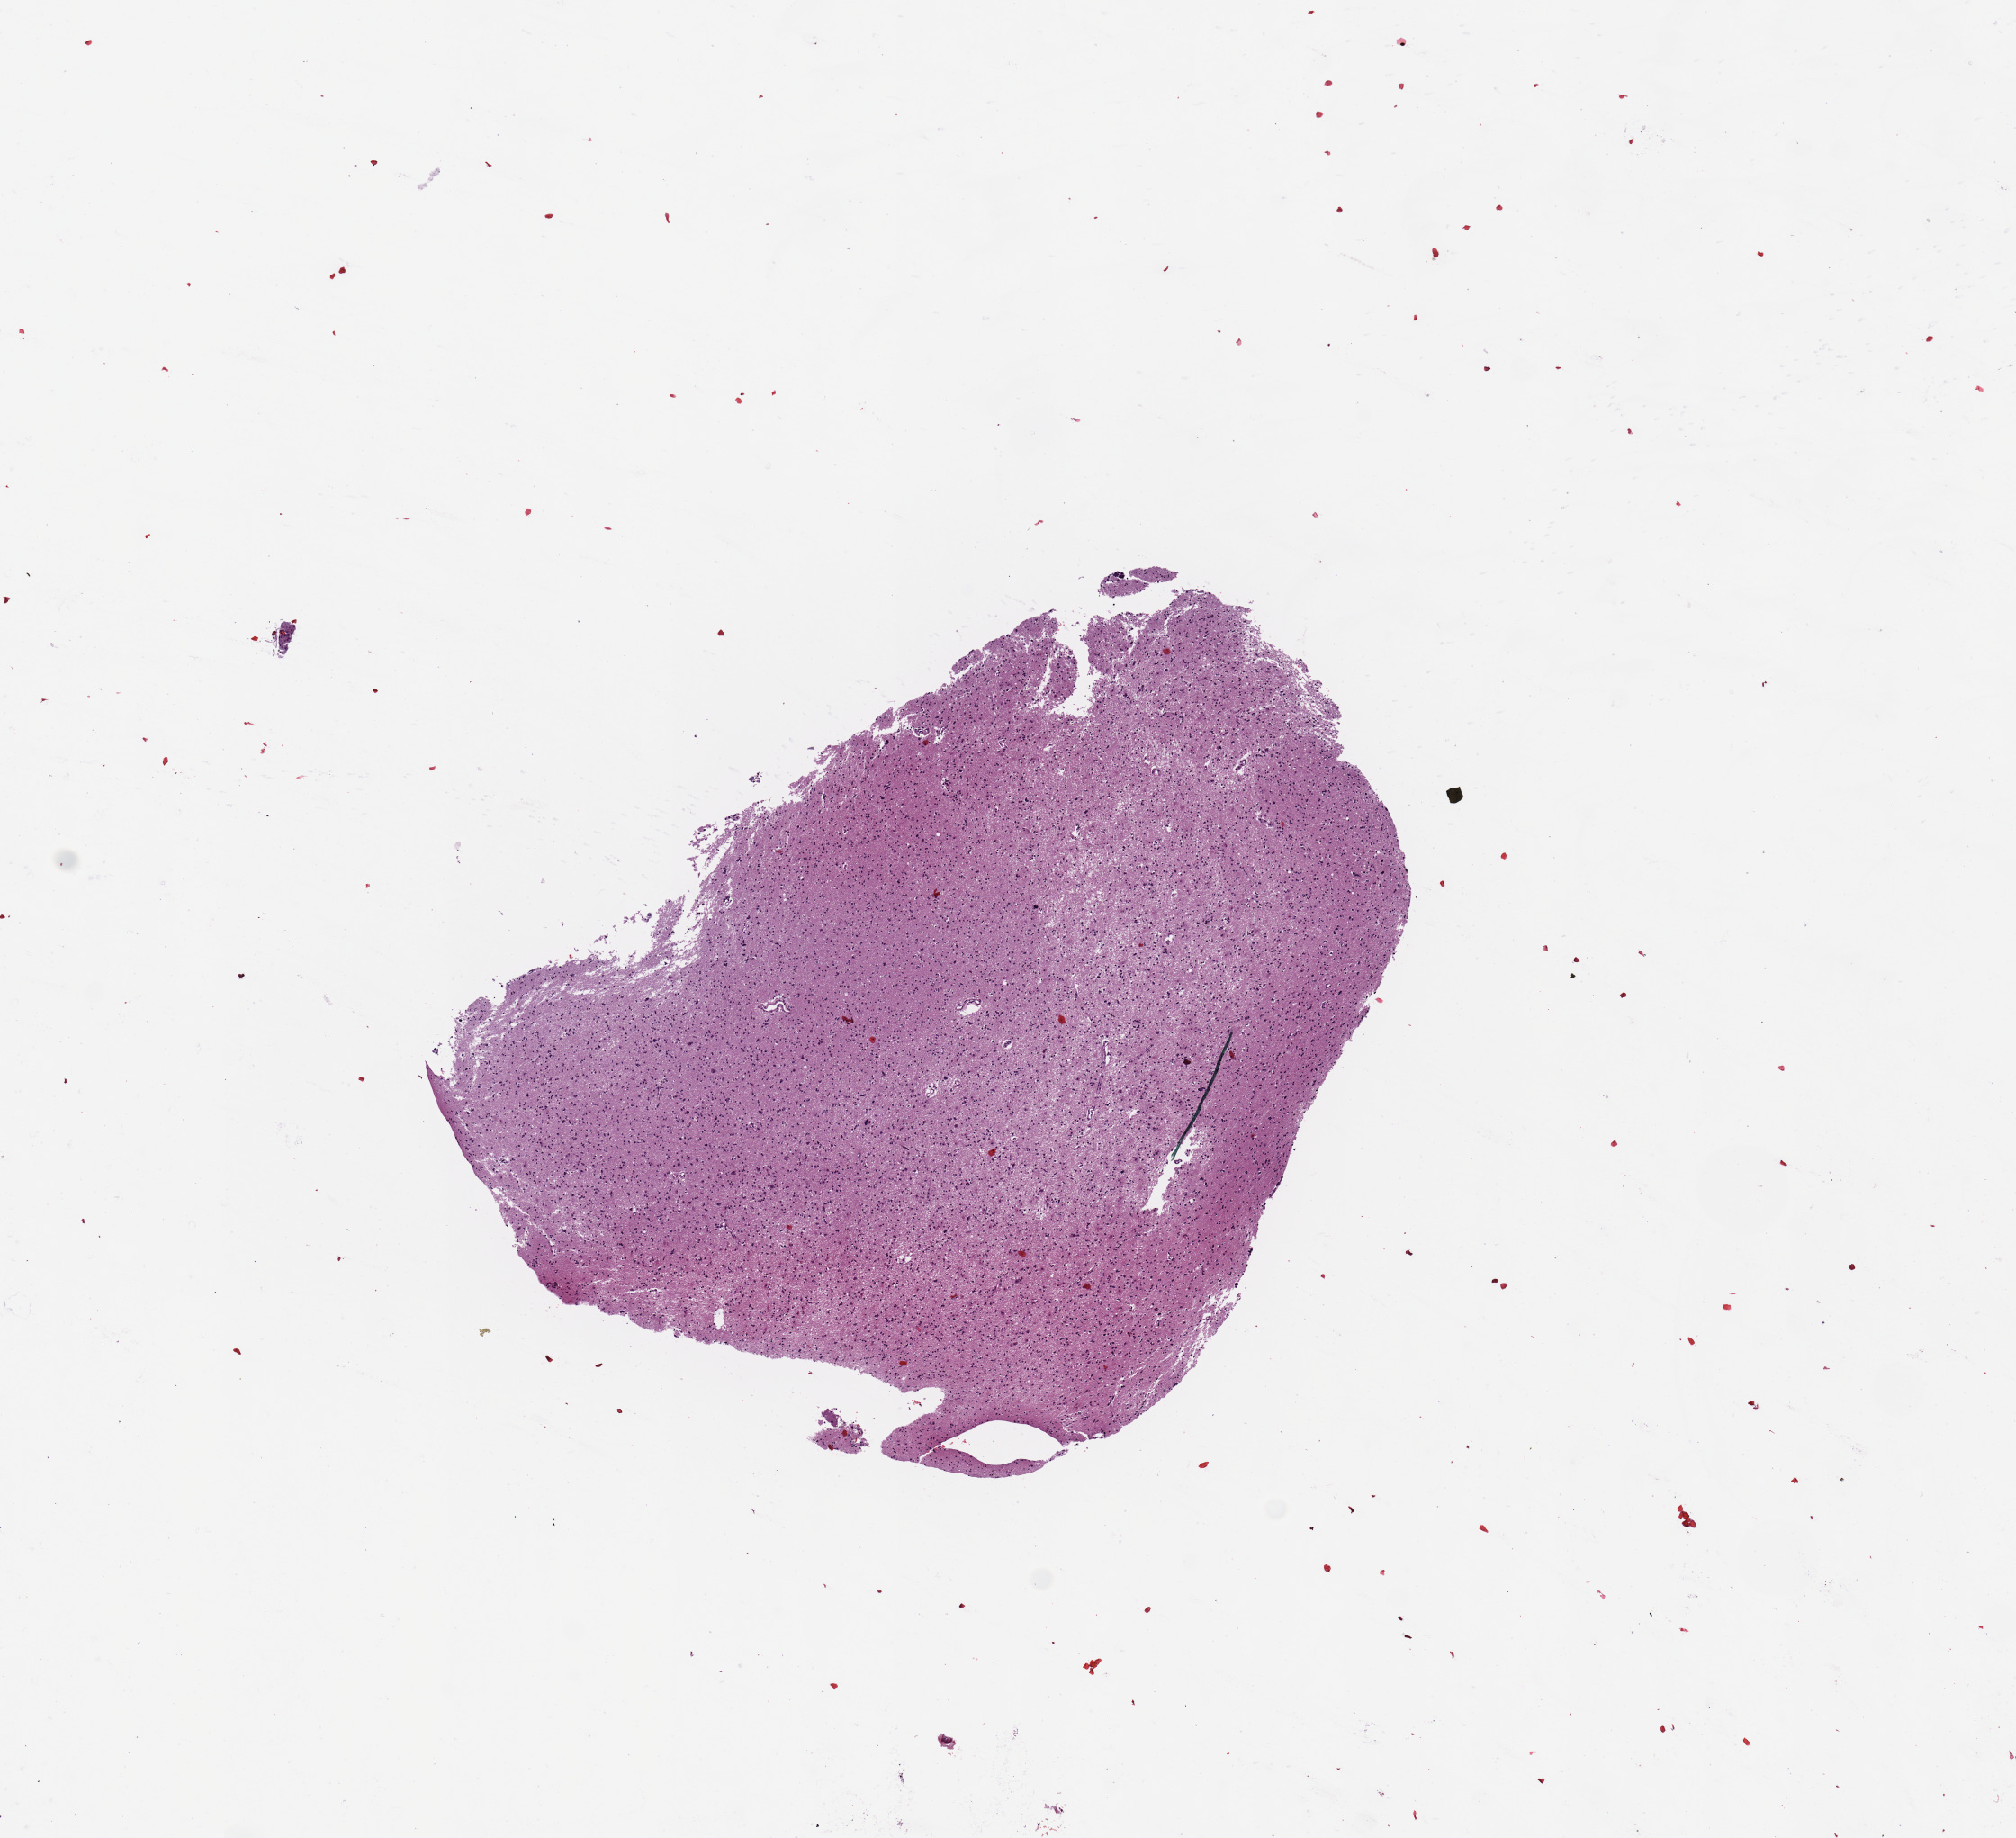
H&E whole-slide image, whole scanned area (about 8.9 x 8.1 mm) shown as a low-resolution overview. Tumour tissue sample, brain. Patient: male, age 43 years.
Patient diagnosis (cohort enrolment): glioblastoma multiforme (brain).